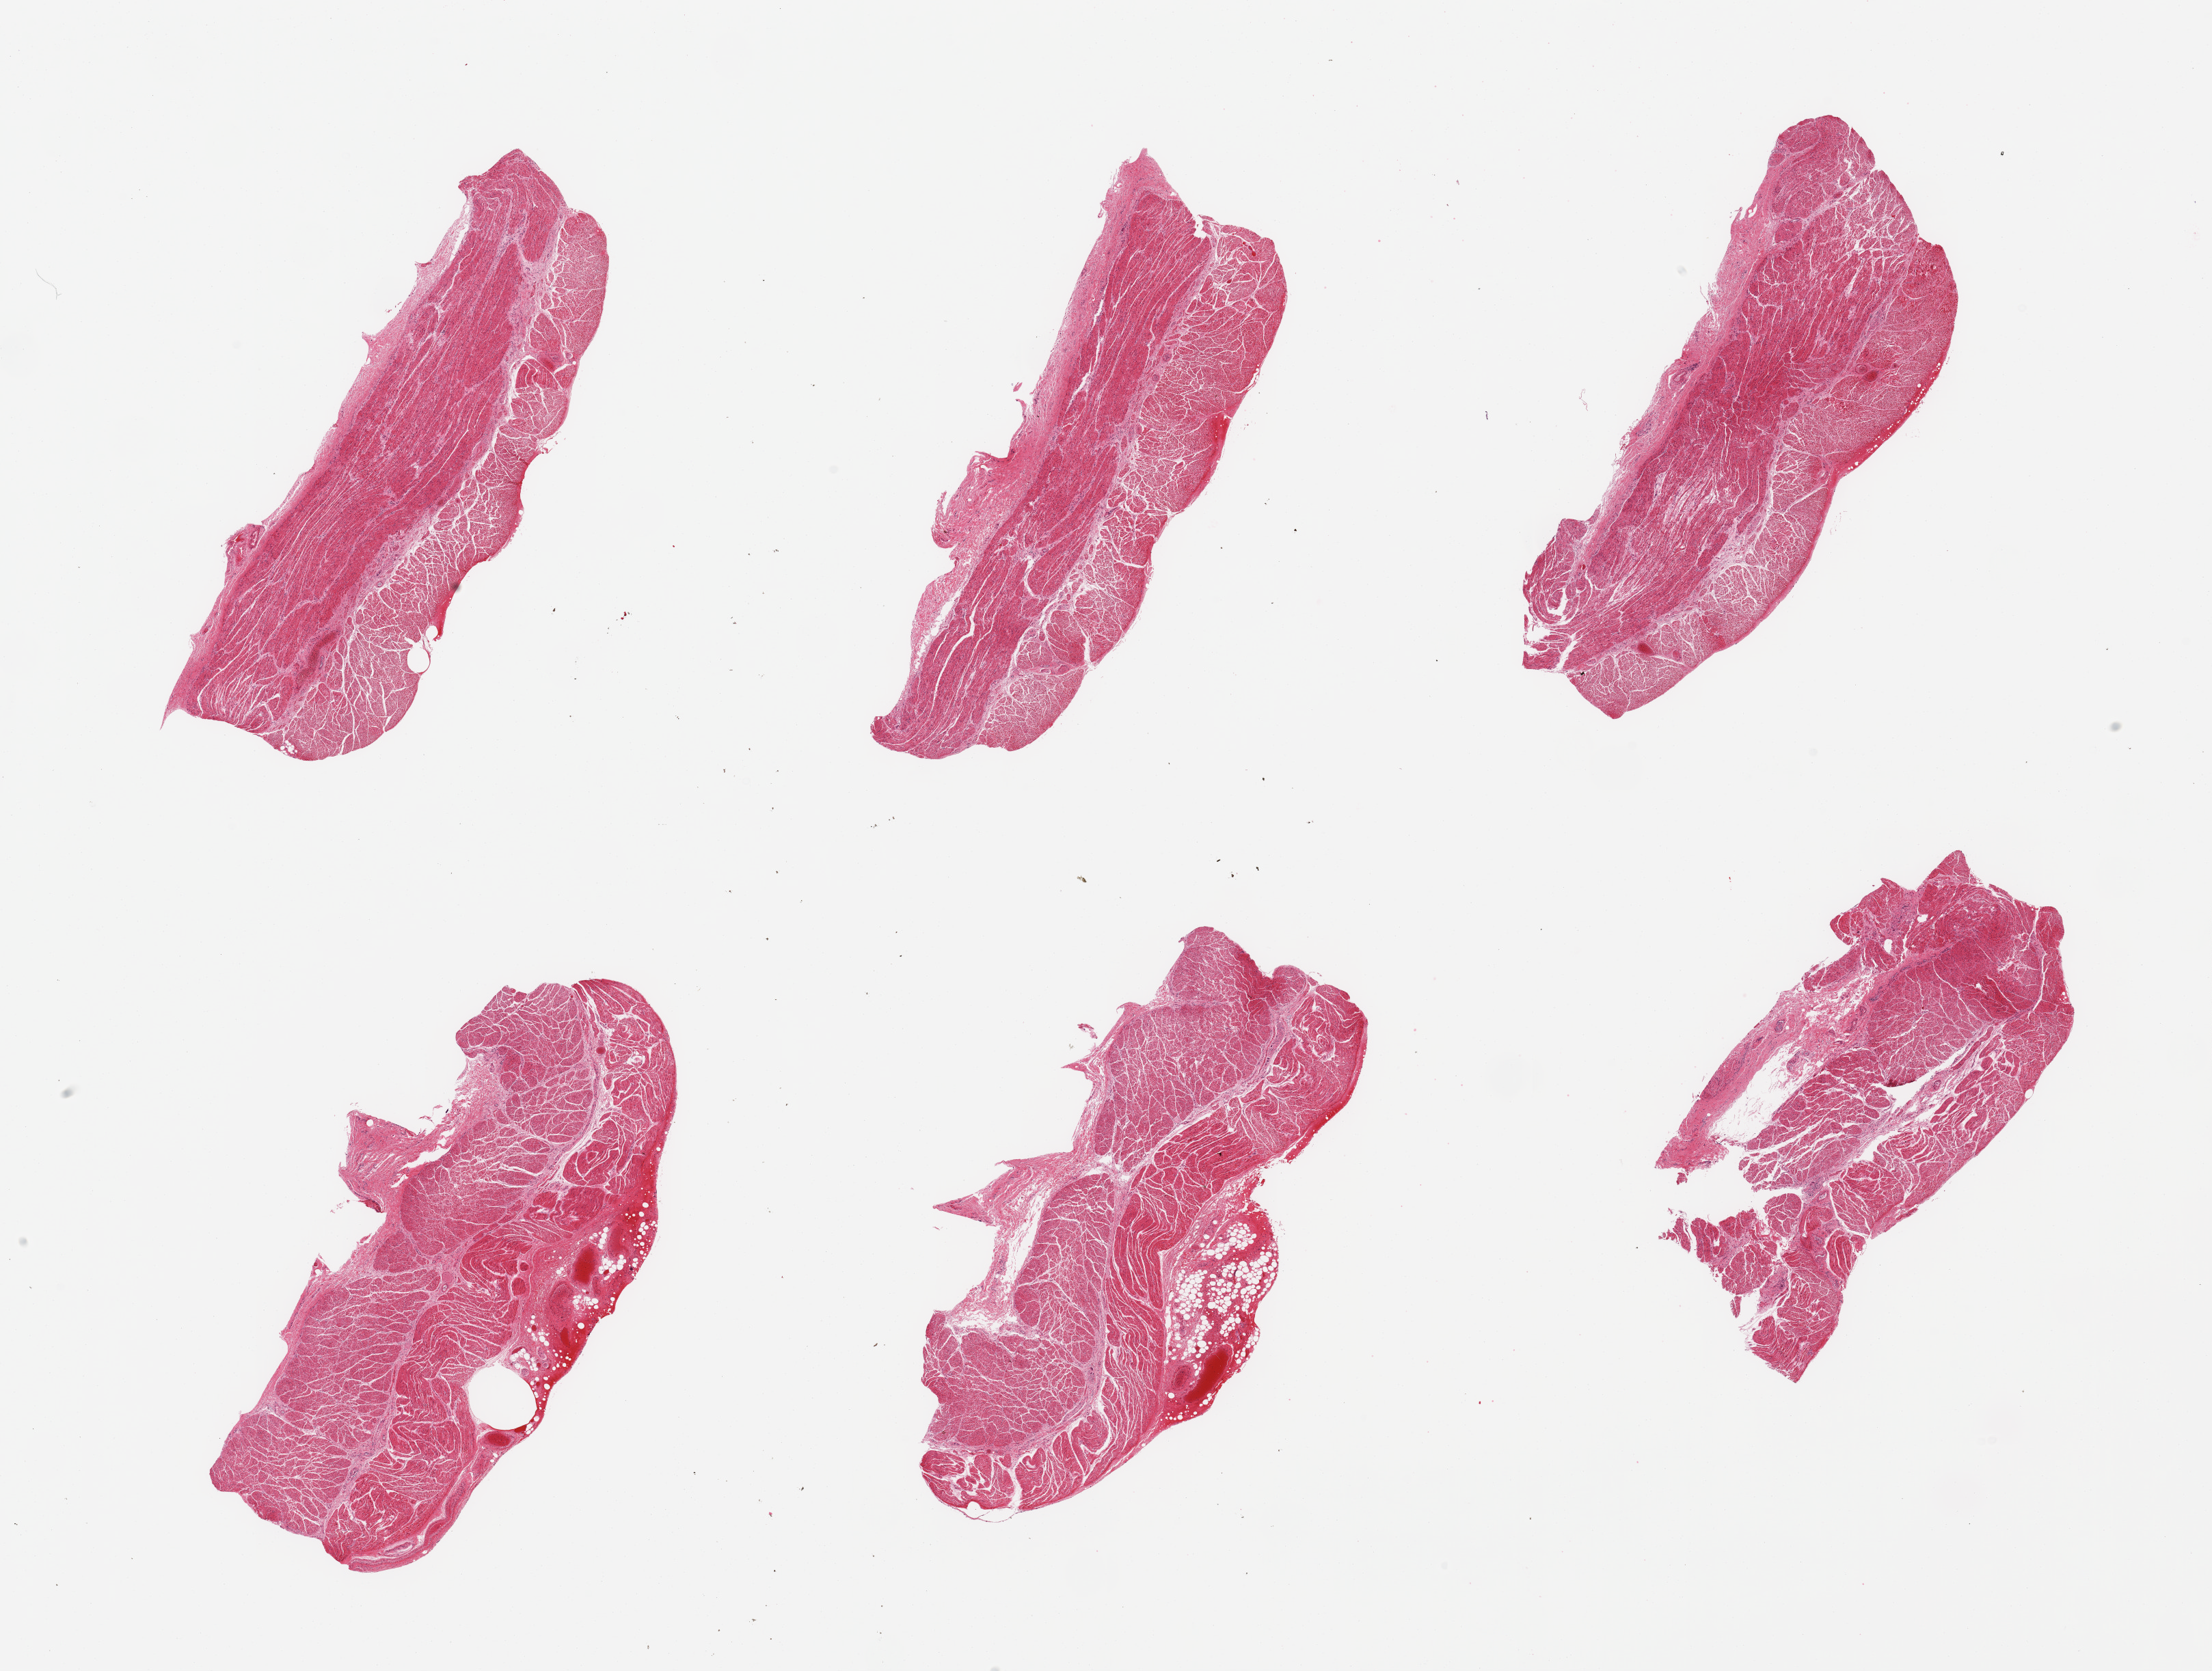
Whole-slide image, hematoxylin and eosin (H&E) stain — shown as a low-resolution overview of the whole scanned area (about 25.6 x 19.3 mm); PAXgene-fixed, paraffin-embedded tissue; section of esophageal muscle (target tissue); tissue donor sample. Donor sex: male.
Review note (as recorded): 6 pieces, confirmed target muscularis.